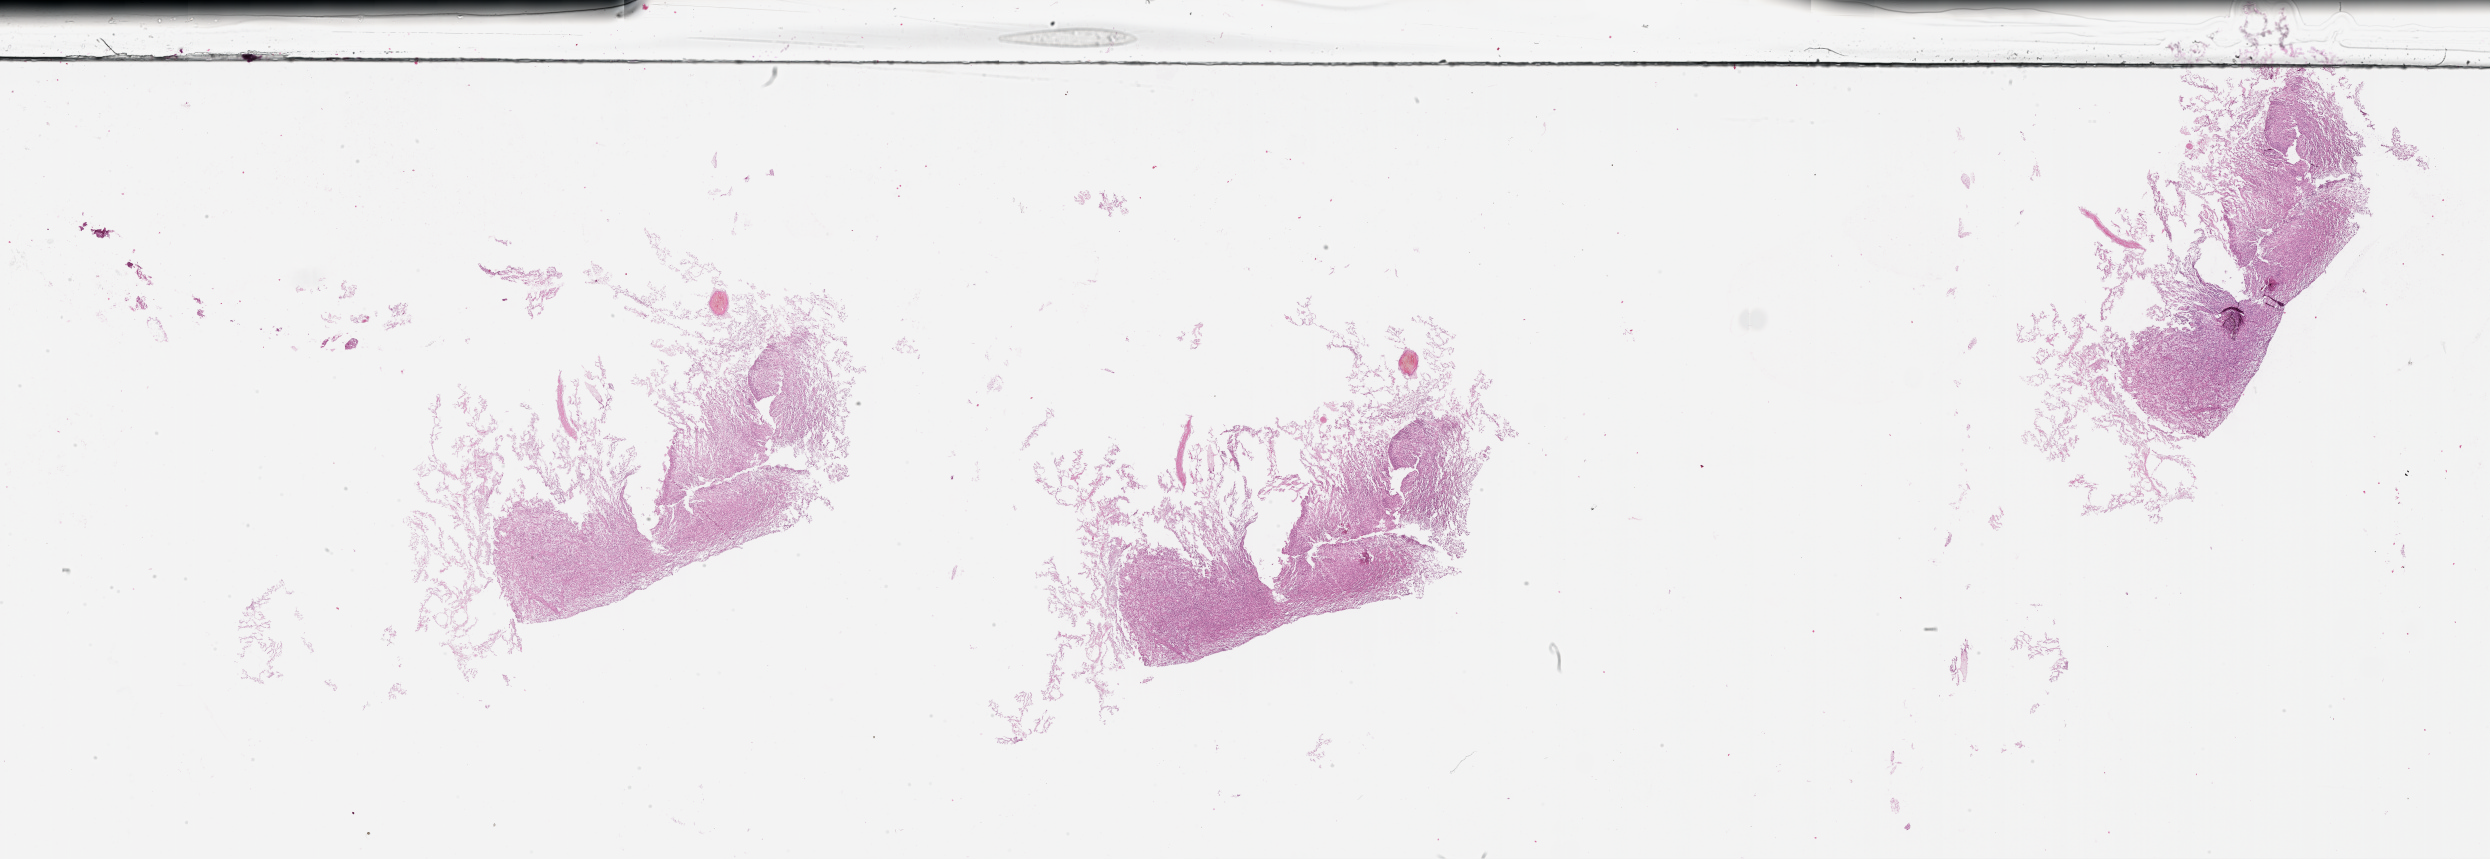
Whole-slide histology image, H&E-stained — shown as a low-resolution overview of the whole scanned area (about 40.1 x 13.8 mm, acquisition: 20x scan); brain, tumour tissue. Male, 58 y/o.
Diagnosis: Glioblastoma. Primary tumour site (as recorded): frontal lobe.